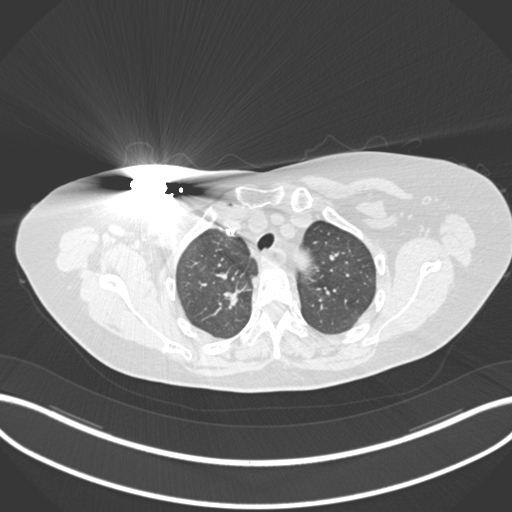
Chest CT, one axial slice; position 146 of 176 along the scan axis; 120 kVp; lung window (W 1500 / L -600 HU); 1 mm slice thickness; 512 × 512 image matrix. Patient: female, 72 years. Case-level facts recorded for this patient, not image findings: clinical TNM (as recorded): T1c N0 M0.
Annotated regions visible in this slice (bounding box drawn by a radiologist):
- lung tumour (recorded histology: adenocarcinoma): bounding box [x1, y1, x2, y2] px = [219, 281, 252, 312]